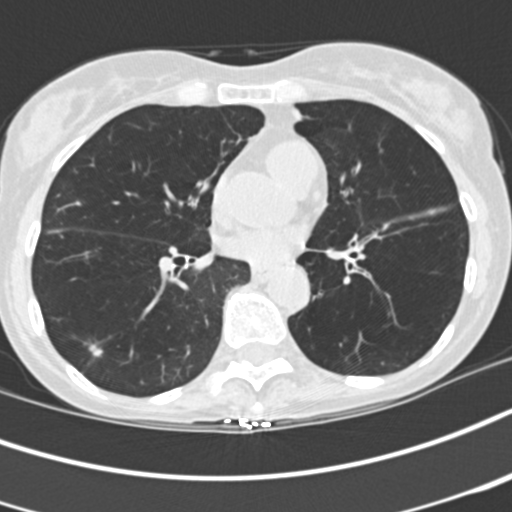
Low-dose screening chest CT, axial slice; baseline annual screen; lung window (W 1500 / L -600 HU); 2 mm slice thickness; slice 100 of 197 in the series. Female participant, aged 68 years at enrolment. Former smoker at enrolment.
Expert reader's lesion annotation, bounding box [x1, y1, x2, y2] px = [75, 339, 114, 368]. The exam's reader record, not a measurement of the box and not confirmed to be the same lesion: non-calcified nodule or mass ≥4 mm, right lower lobe, 8 × 4 mm, spiculated (stellate) margins, soft tissue attenuation. Lung cancer was diagnosed 1012 days after this screen (after the third annual screen): squamous cell carcinoma, NOS, right lower lobe, stage IA (AJCC 6th edition).